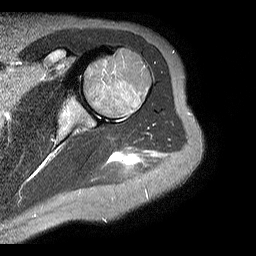
MRI of an extremity soft-tissue mass, one axial slice. Position 14 of 20 along the scan axis. STIR. 4 mm slice thickness. 256 × 256 image matrix, field of view 150 × 150 mm. Female patient. Case-level facts recorded for this patient, not image findings: histological type: malignant fibrous histiocytoma; grade: low; site of the primary tumour: left arm.
Structures marked on this image (expert manual segmentation):
- gross tumour volume (mass): bounding box (x1, y1, x2, y2) in pixels: (113, 151, 135, 162)